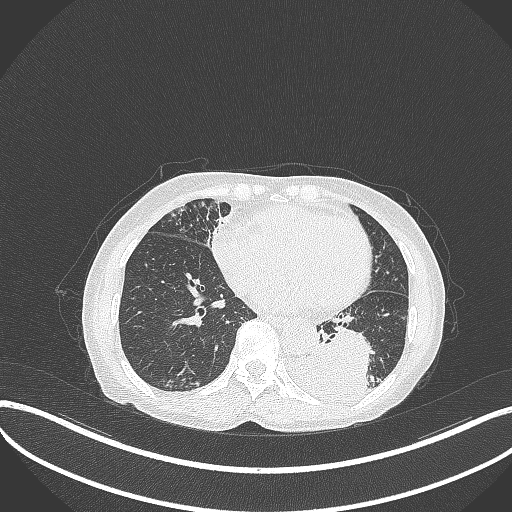
Chest CT, one axial slice; reconstruction kernel B70f; 120 kVp; lung window (W 1500 / L -600 HU); 1 mm slice thickness; 512 × 512 image matrix, field of view 400 × 400 mm. Patient: female, 78 years. Case-level facts recorded for this patient, not image findings: clinical TNM (as recorded): T3 N0 M1.
Annotated regions visible in this slice (bounding box drawn by a radiologist):
- lung tumour (recorded histology: squamous cell carcinoma): bounding box [x1, y1, x2, y2] px = [281, 327, 373, 408]